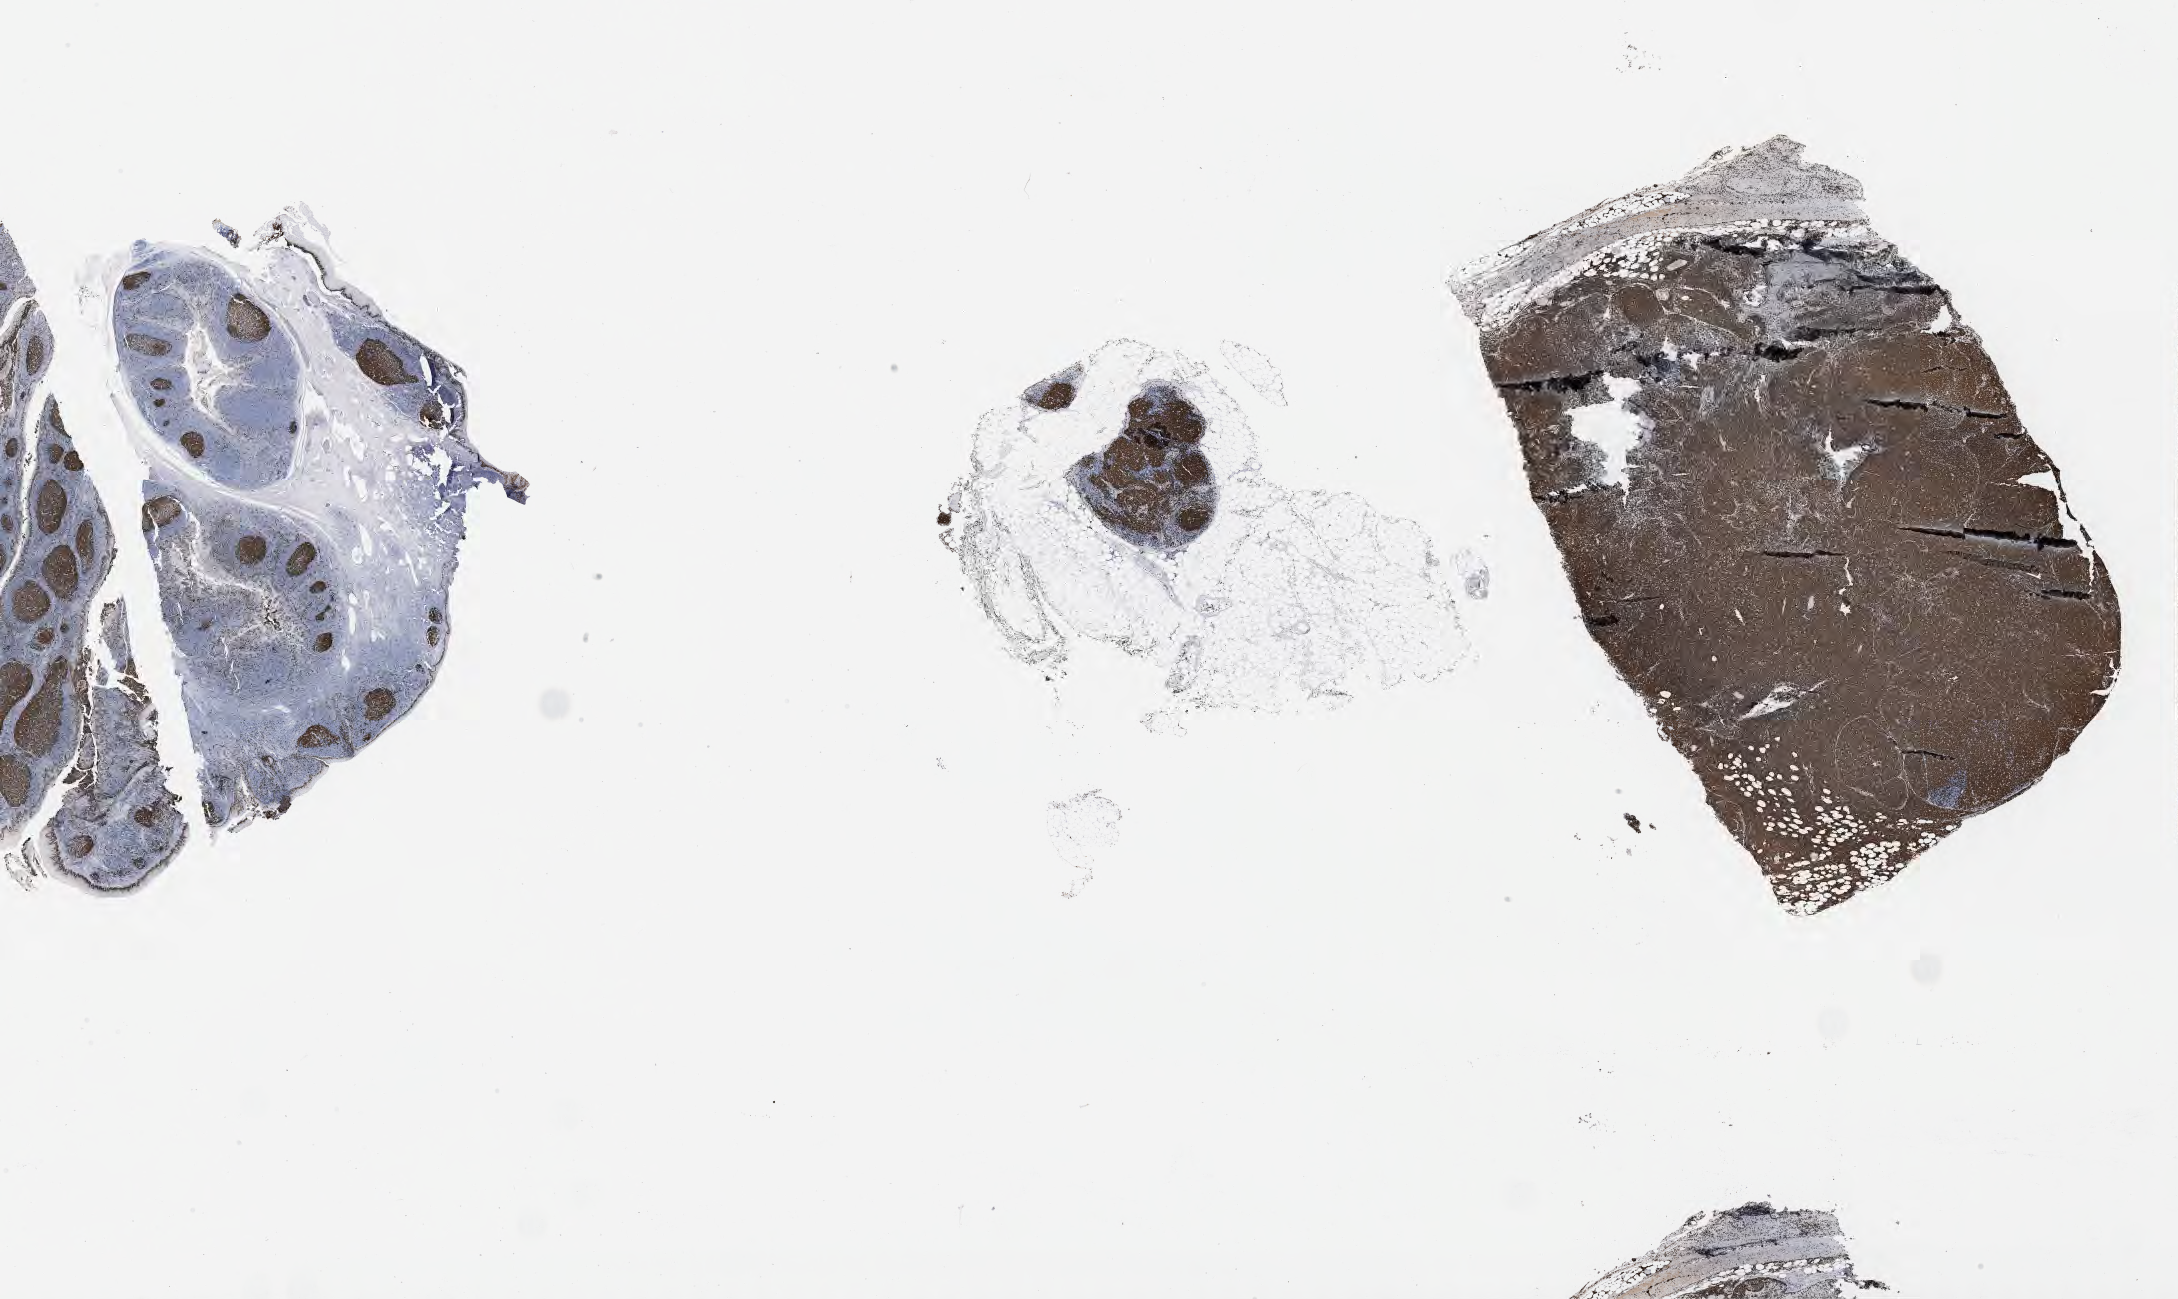
Immunohistochemistry (IHC) whole-slide image stained for Ki-67, shown as a low-resolution overview of the whole scanned area (about 35.2 x 21.0 mm). Tumor tissue. Male patient, 40 years old.
Diagnosis: Burkitt lymphoma, NOS.